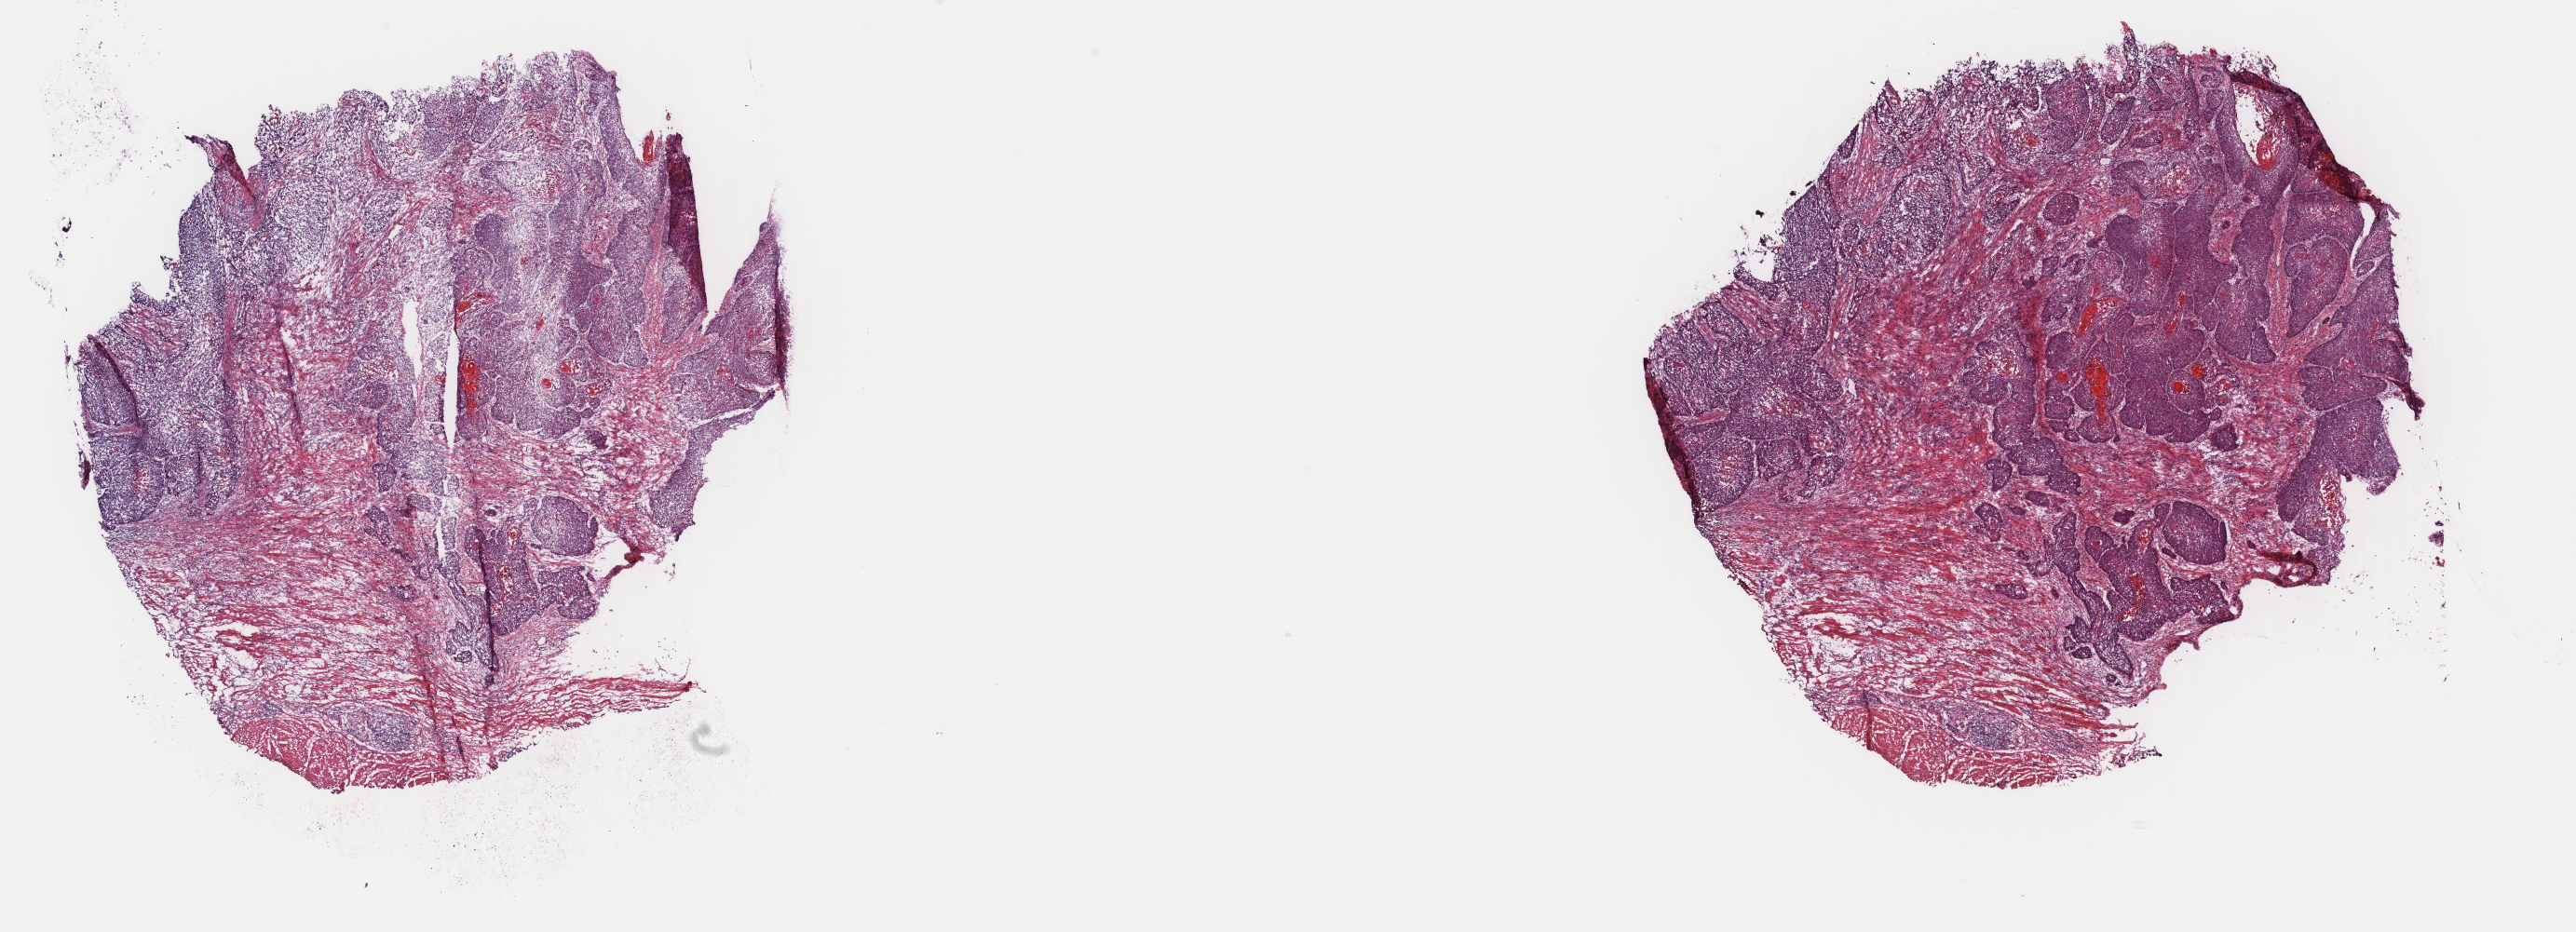
Digitized H&E-stained tissue section (whole slide), shown as a low-resolution overview of the whole scanned area (about 22.0 x 7.9 mm, slide scanned at 40x); frozen section; esophagus, primary tumour sample. Male patient; age at initial diagnosis 72 years. Histologic grade: G2 (moderately differentiated). Slide review estimates, as recorded: tumour cells 46%, tumour nuclei 80%, normal cells 0%, stromal cells 45%, necrosis 9%. Infiltration values recorded for this section: lymphocyte infiltration 14%, monocyte infiltration 0%, neutrophil infiltration 1%.
Pathologic diagnosis: Squamous cell carcinoma, NOS. AJCC pathologic stage: IIA.